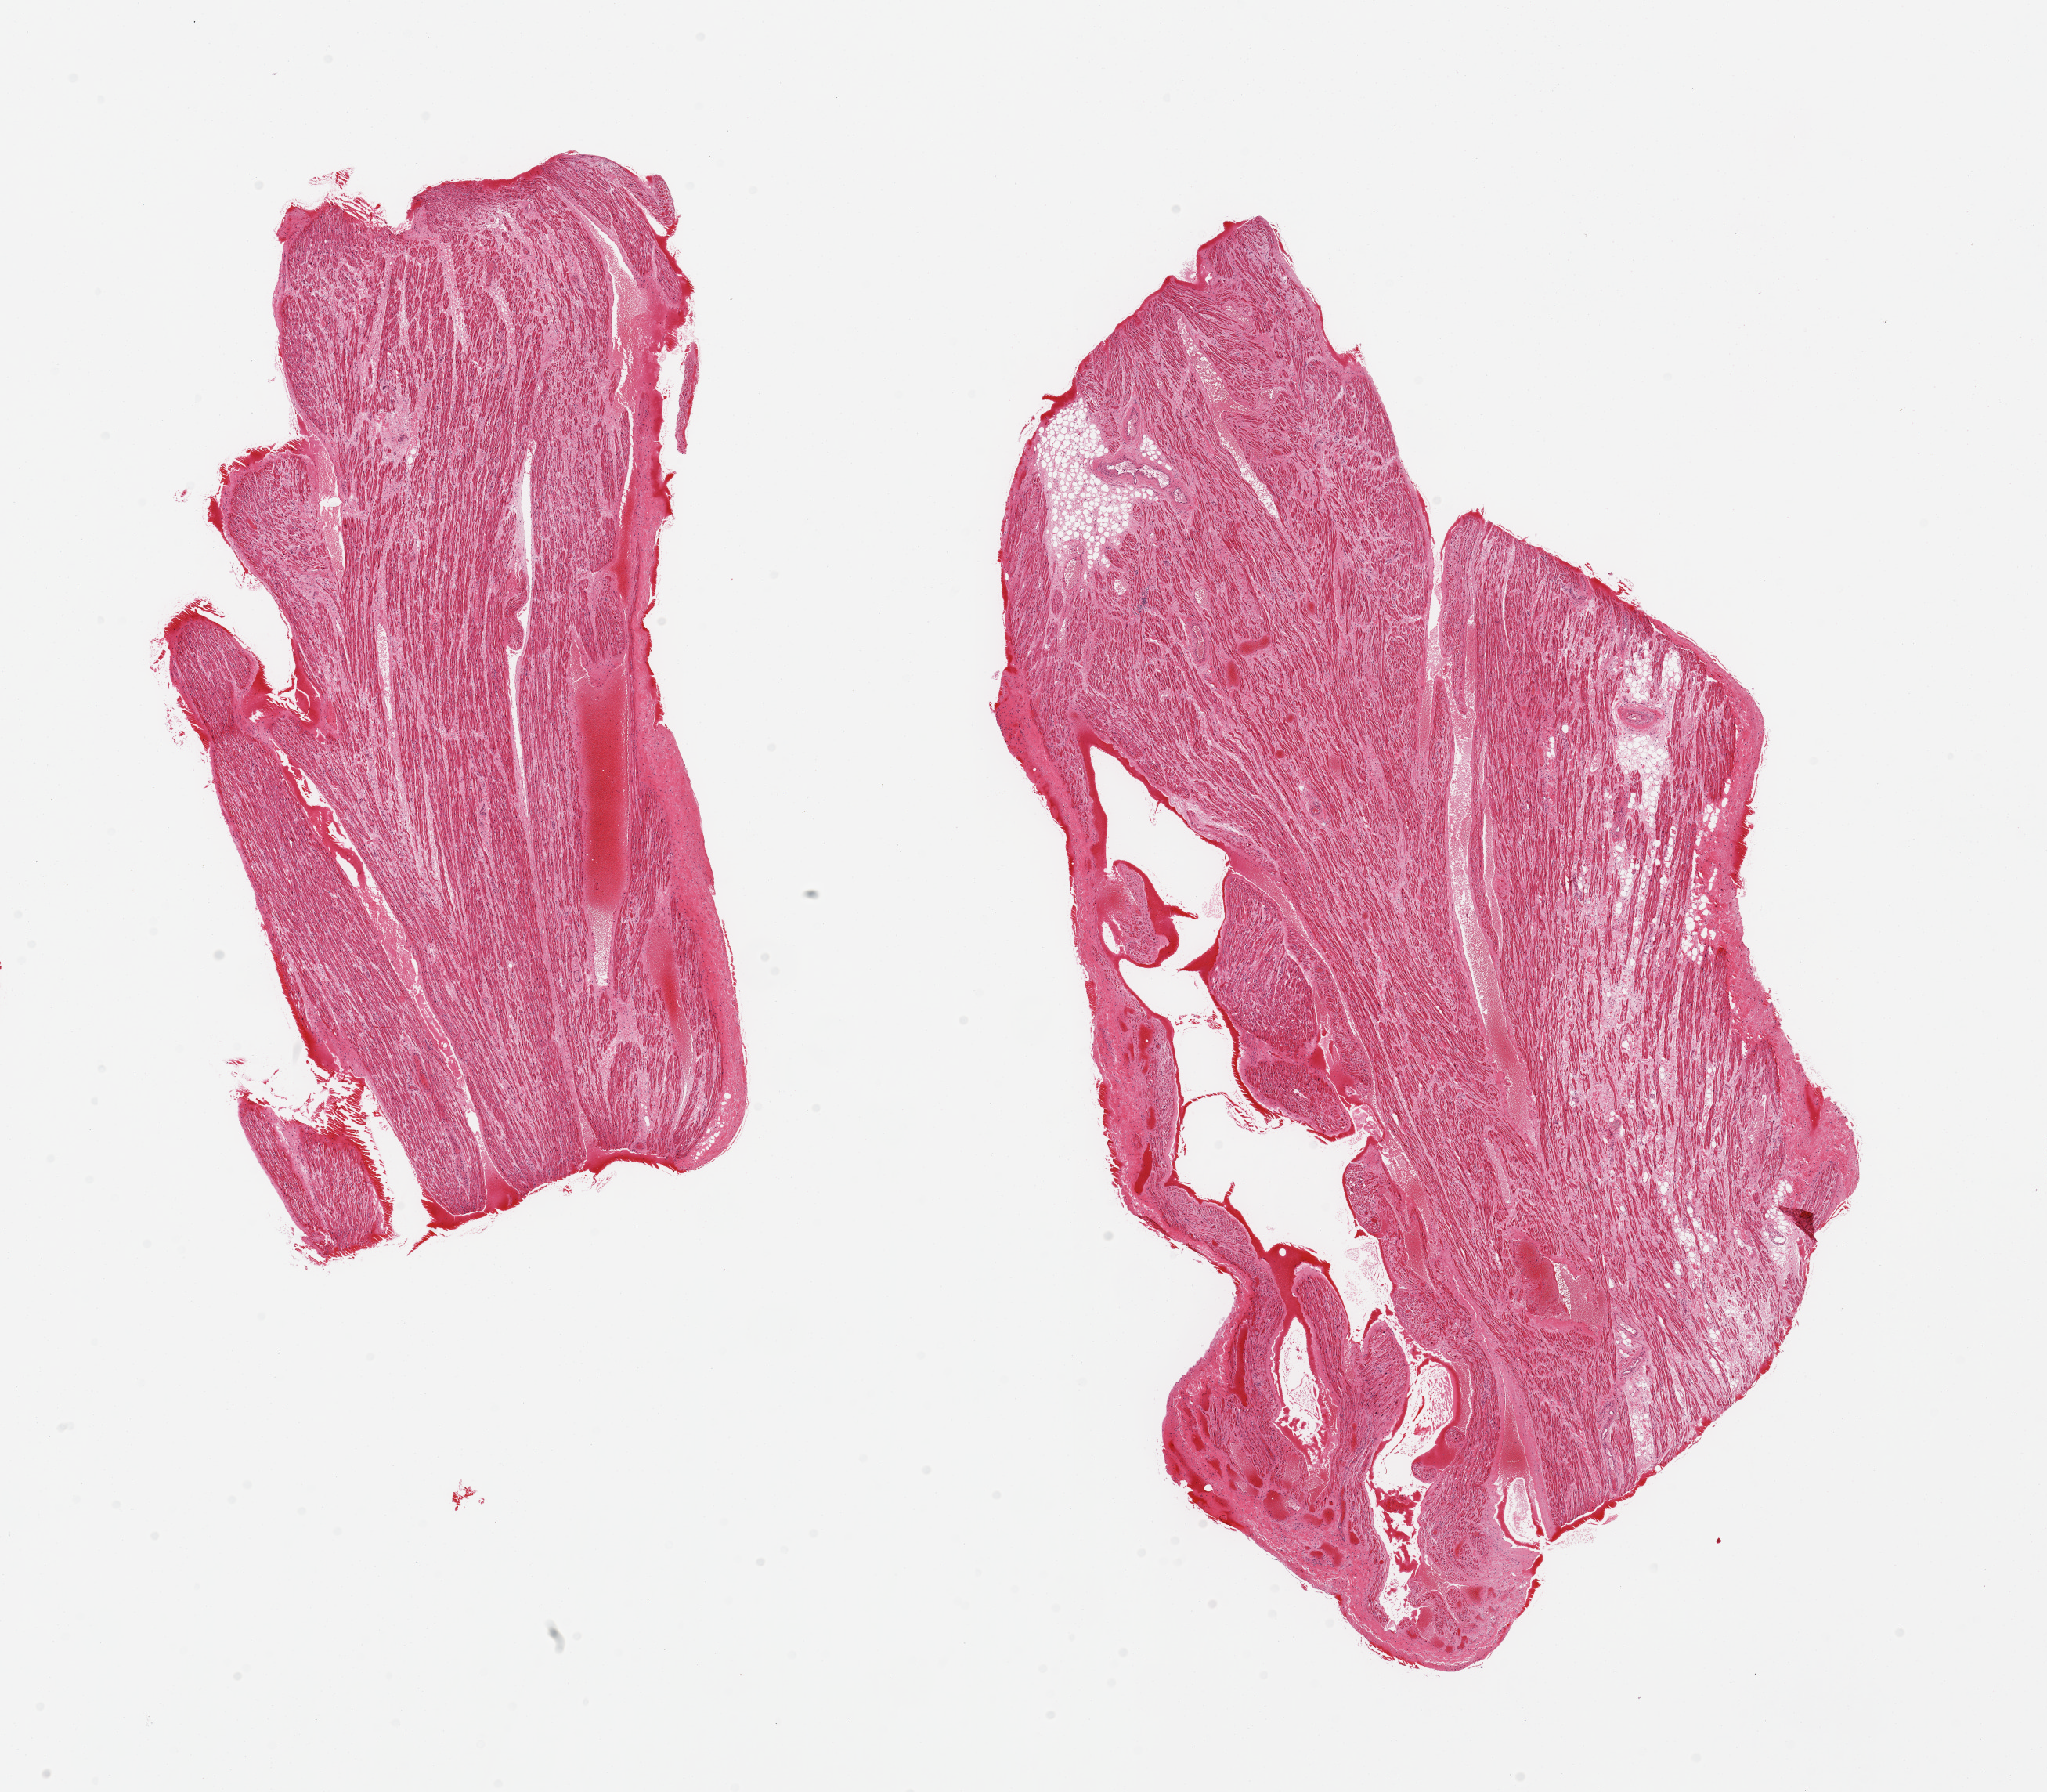
Digitized H&E-stained section, low-resolution overview of the scanned area, about 20.7 x 18.1 mm (from a 20x scan); PAXgene-fixed, paraffin-embedded tissue; section of auricular appendage (target tissue); tissue donor sample. Male donor.
Pathologist's review note for this sample: 2 pieces; interstitial fibrosis and fat with congestion.